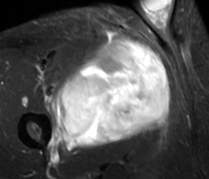
MRI of an extremity soft-tissue mass, one axial slice; STIR; MR volume resampled by the dataset authors to the PET/CT grid (not the native acquisition matrix); 3.27 mm slice thickness; 209 × 179 image matrix, field of view 204 × 175 mm. Male patient. From the clinical record (not read from this slice): histological type: undifferentiated - pleiomorphic; grade: high; site of the primary tumour: right thigh.
Outlined on this slice (expert contour drawn on MRI and transferred to this co-registered scan by the dataset authors):
- gross tumour volume including surrounding oedema: bounding box [x1, y1, x2, y2] px = [48, 37, 170, 150]
- gross tumour volume (mass): [57, 39, 170, 149]